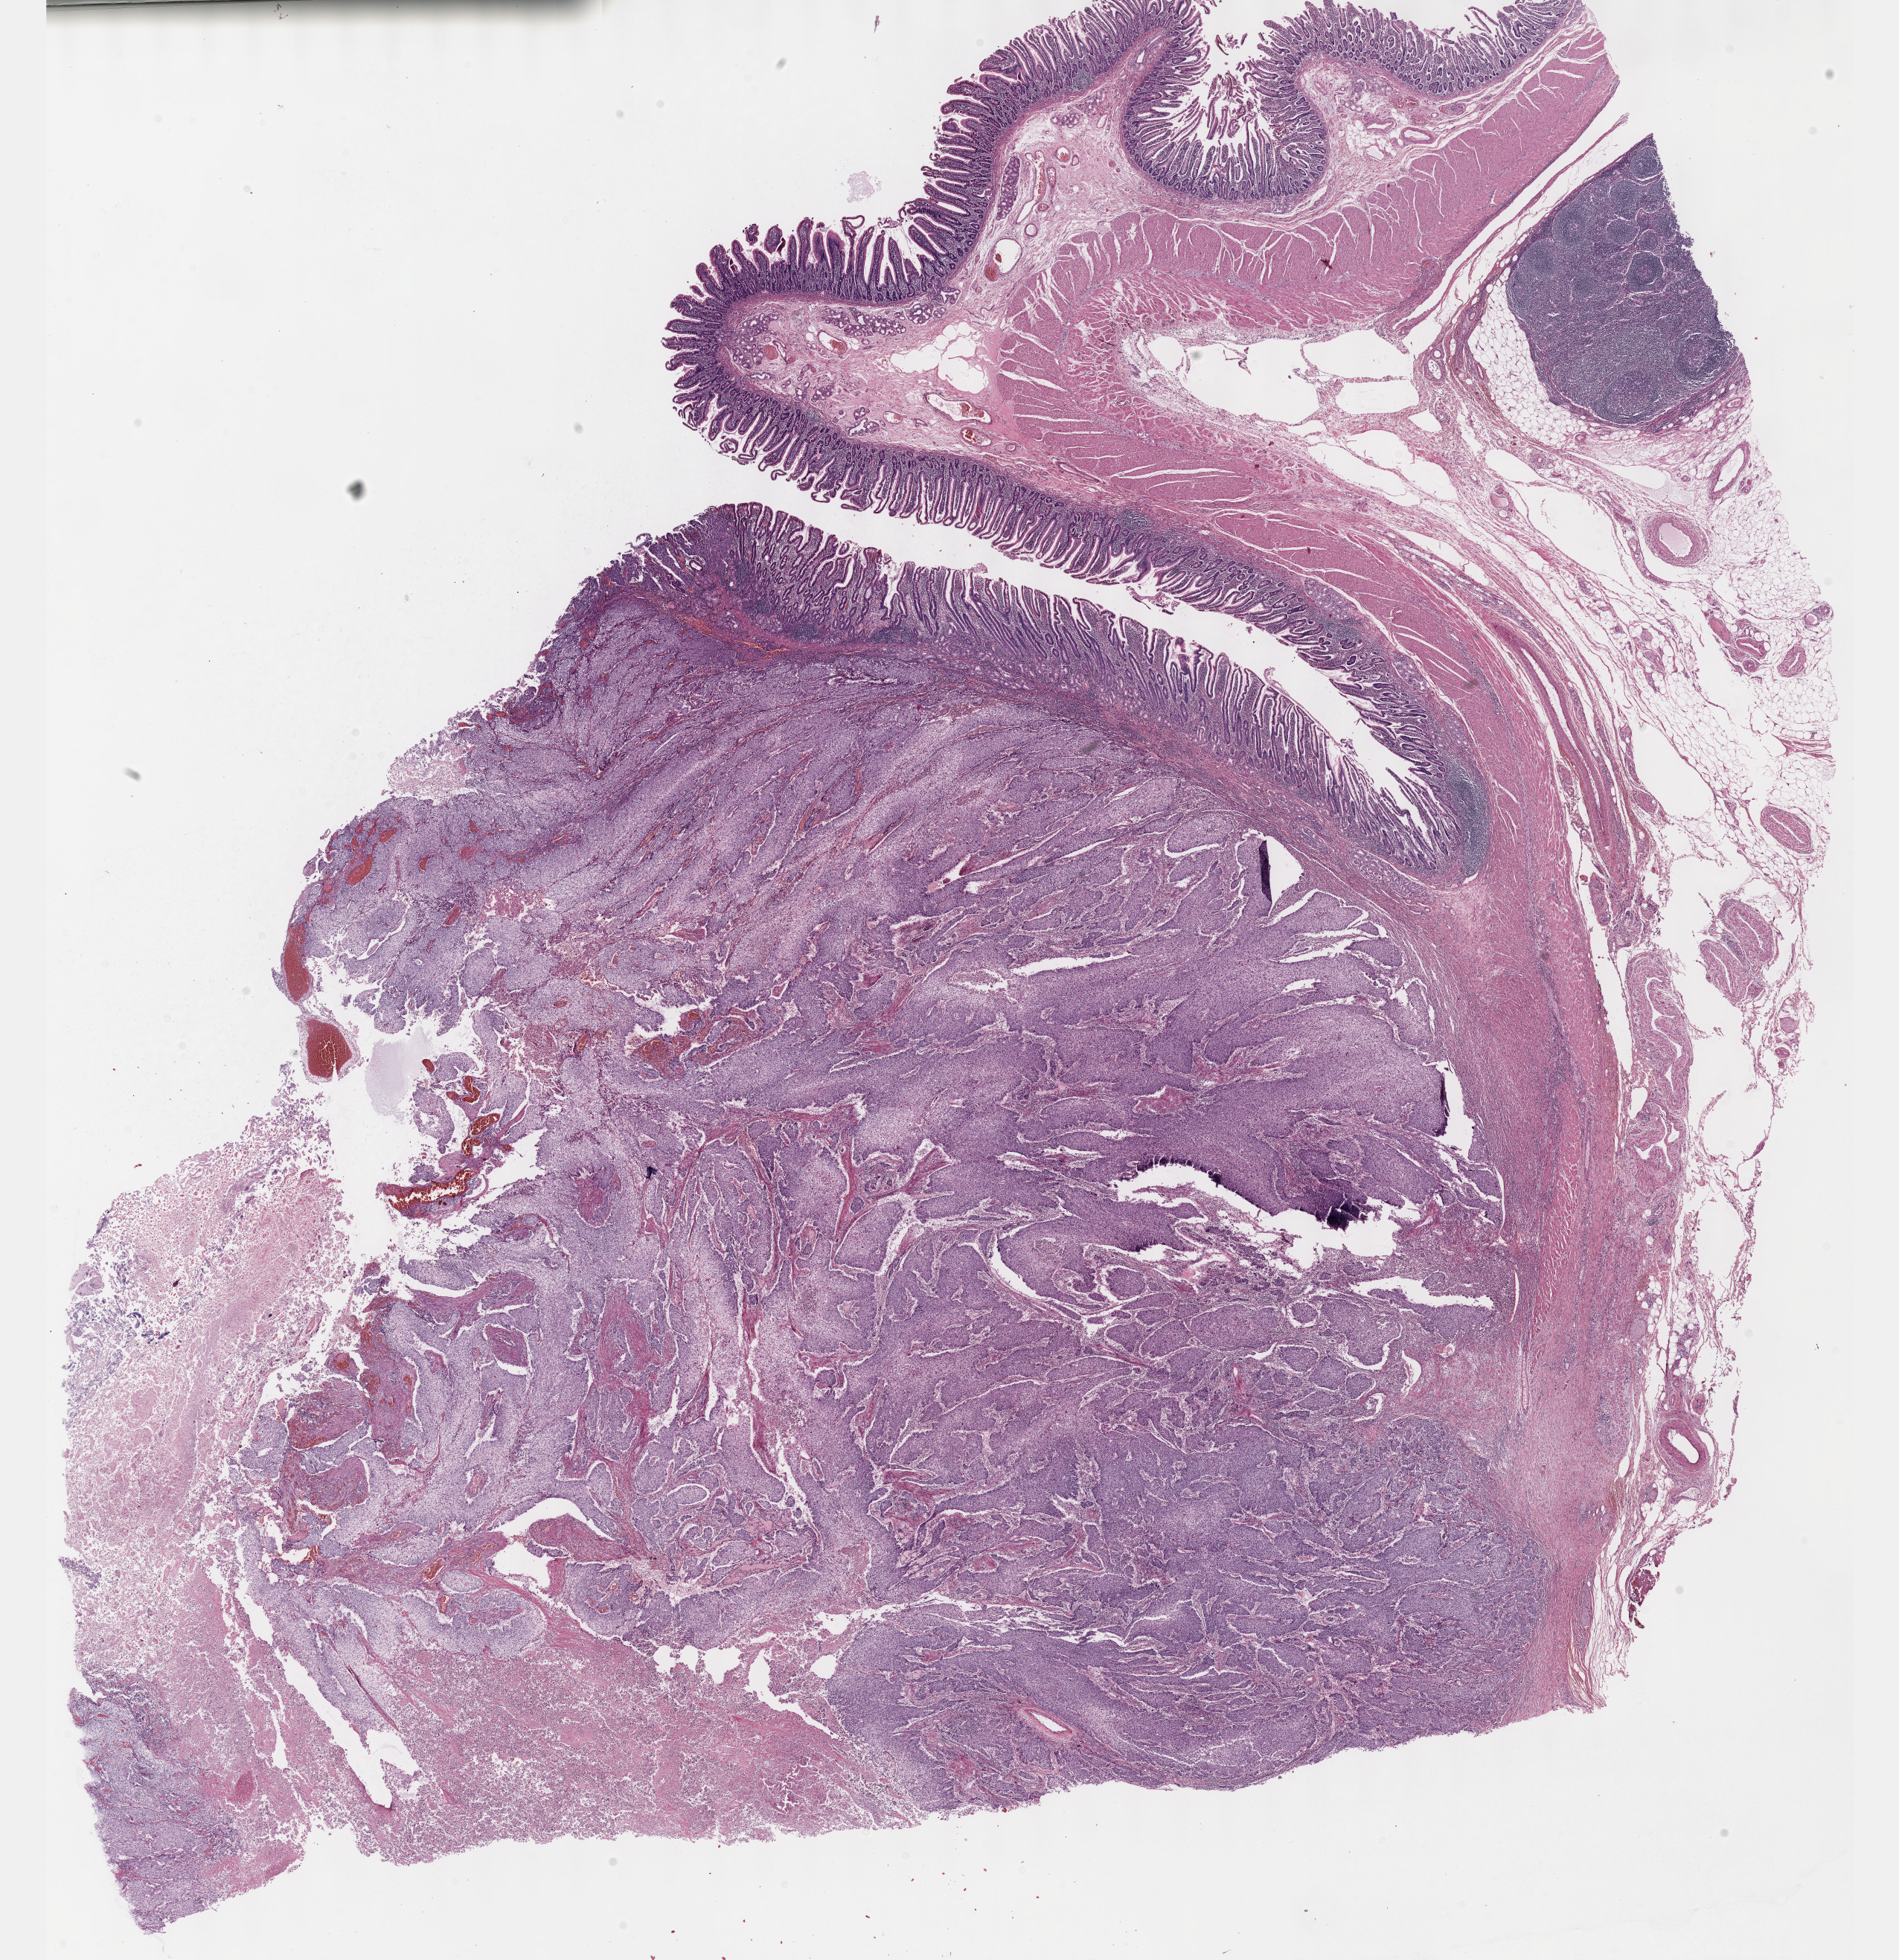
Digitized H&E-stained tissue section (whole slide), a low-resolution overview of the entire scanned area, about 20.6 x 21.3 mm; formalin-fixed paraffin-embedded (FFPE) diagnostic section; sample: primary tumour, stomach. Patient: female, age at initial diagnosis 67 years. Histologic grade: G3 (poorly differentiated).
• AJCC pathologic stage: IIIB
• pathologic diagnosis: Adenocarcinoma, intestinal type (gastric antrum)
• lymph nodes positive (case pathology): 0 of 29 examined